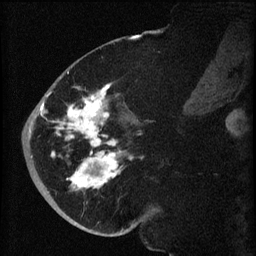
Breast MRI (dynamic contrast-enhanced), one sagittal slice; dynamic contrast-enhanced series, image 2 of 3 at this slice position (ordered by acquisition); 1.5 T; TE 4.2 ms, TR 8.2 ms; 256 × 256 image matrix, field of view 180 × 180 mm. Female patient, age 71 years.
Annotated regions visible in this slice (semi-automatically segmented with operator editing):
- analysis volume of interest (the breast-tissue region the enhancement analysis was run in; not a lesion): bounding box [x1, y1, x2, y2] px = [40, 72, 140, 196]
- tumour enhancement mask (voxels above the 70 % enhancement threshold inside the analysis volume of interest): [40, 72, 132, 190]